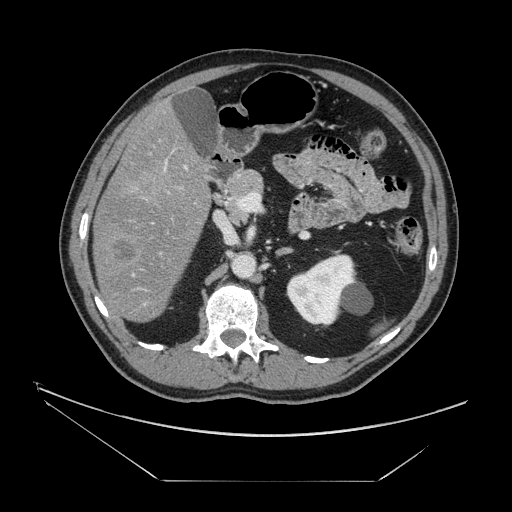
Contrast-enhanced abdominal CT, one axial slice; position 75 of 161 along the scan axis; 120 kVp; intravenous contrast given; soft-tissue window (W 400 / L 40 HU); 2.5 mm slice thickness; 512 × 512 image matrix, field of view 440 × 440 mm. Male patient, age 65 years. Case-level facts recorded for this patient, not image findings: diagnosis: colorectal cancer liver metastases, imaged before liver resection; multiple liver metastases: yes; largest metastasis: 4.2 cm.
Outlined on this slice (manually delineated by an expert):
- liver: bounding box <94,106,210,322> (left, top, right, bottom; pixels)
- portal vein (with intrahepatic branches): <165,162,186,169>
- liver metastasis: <117,244,134,261>